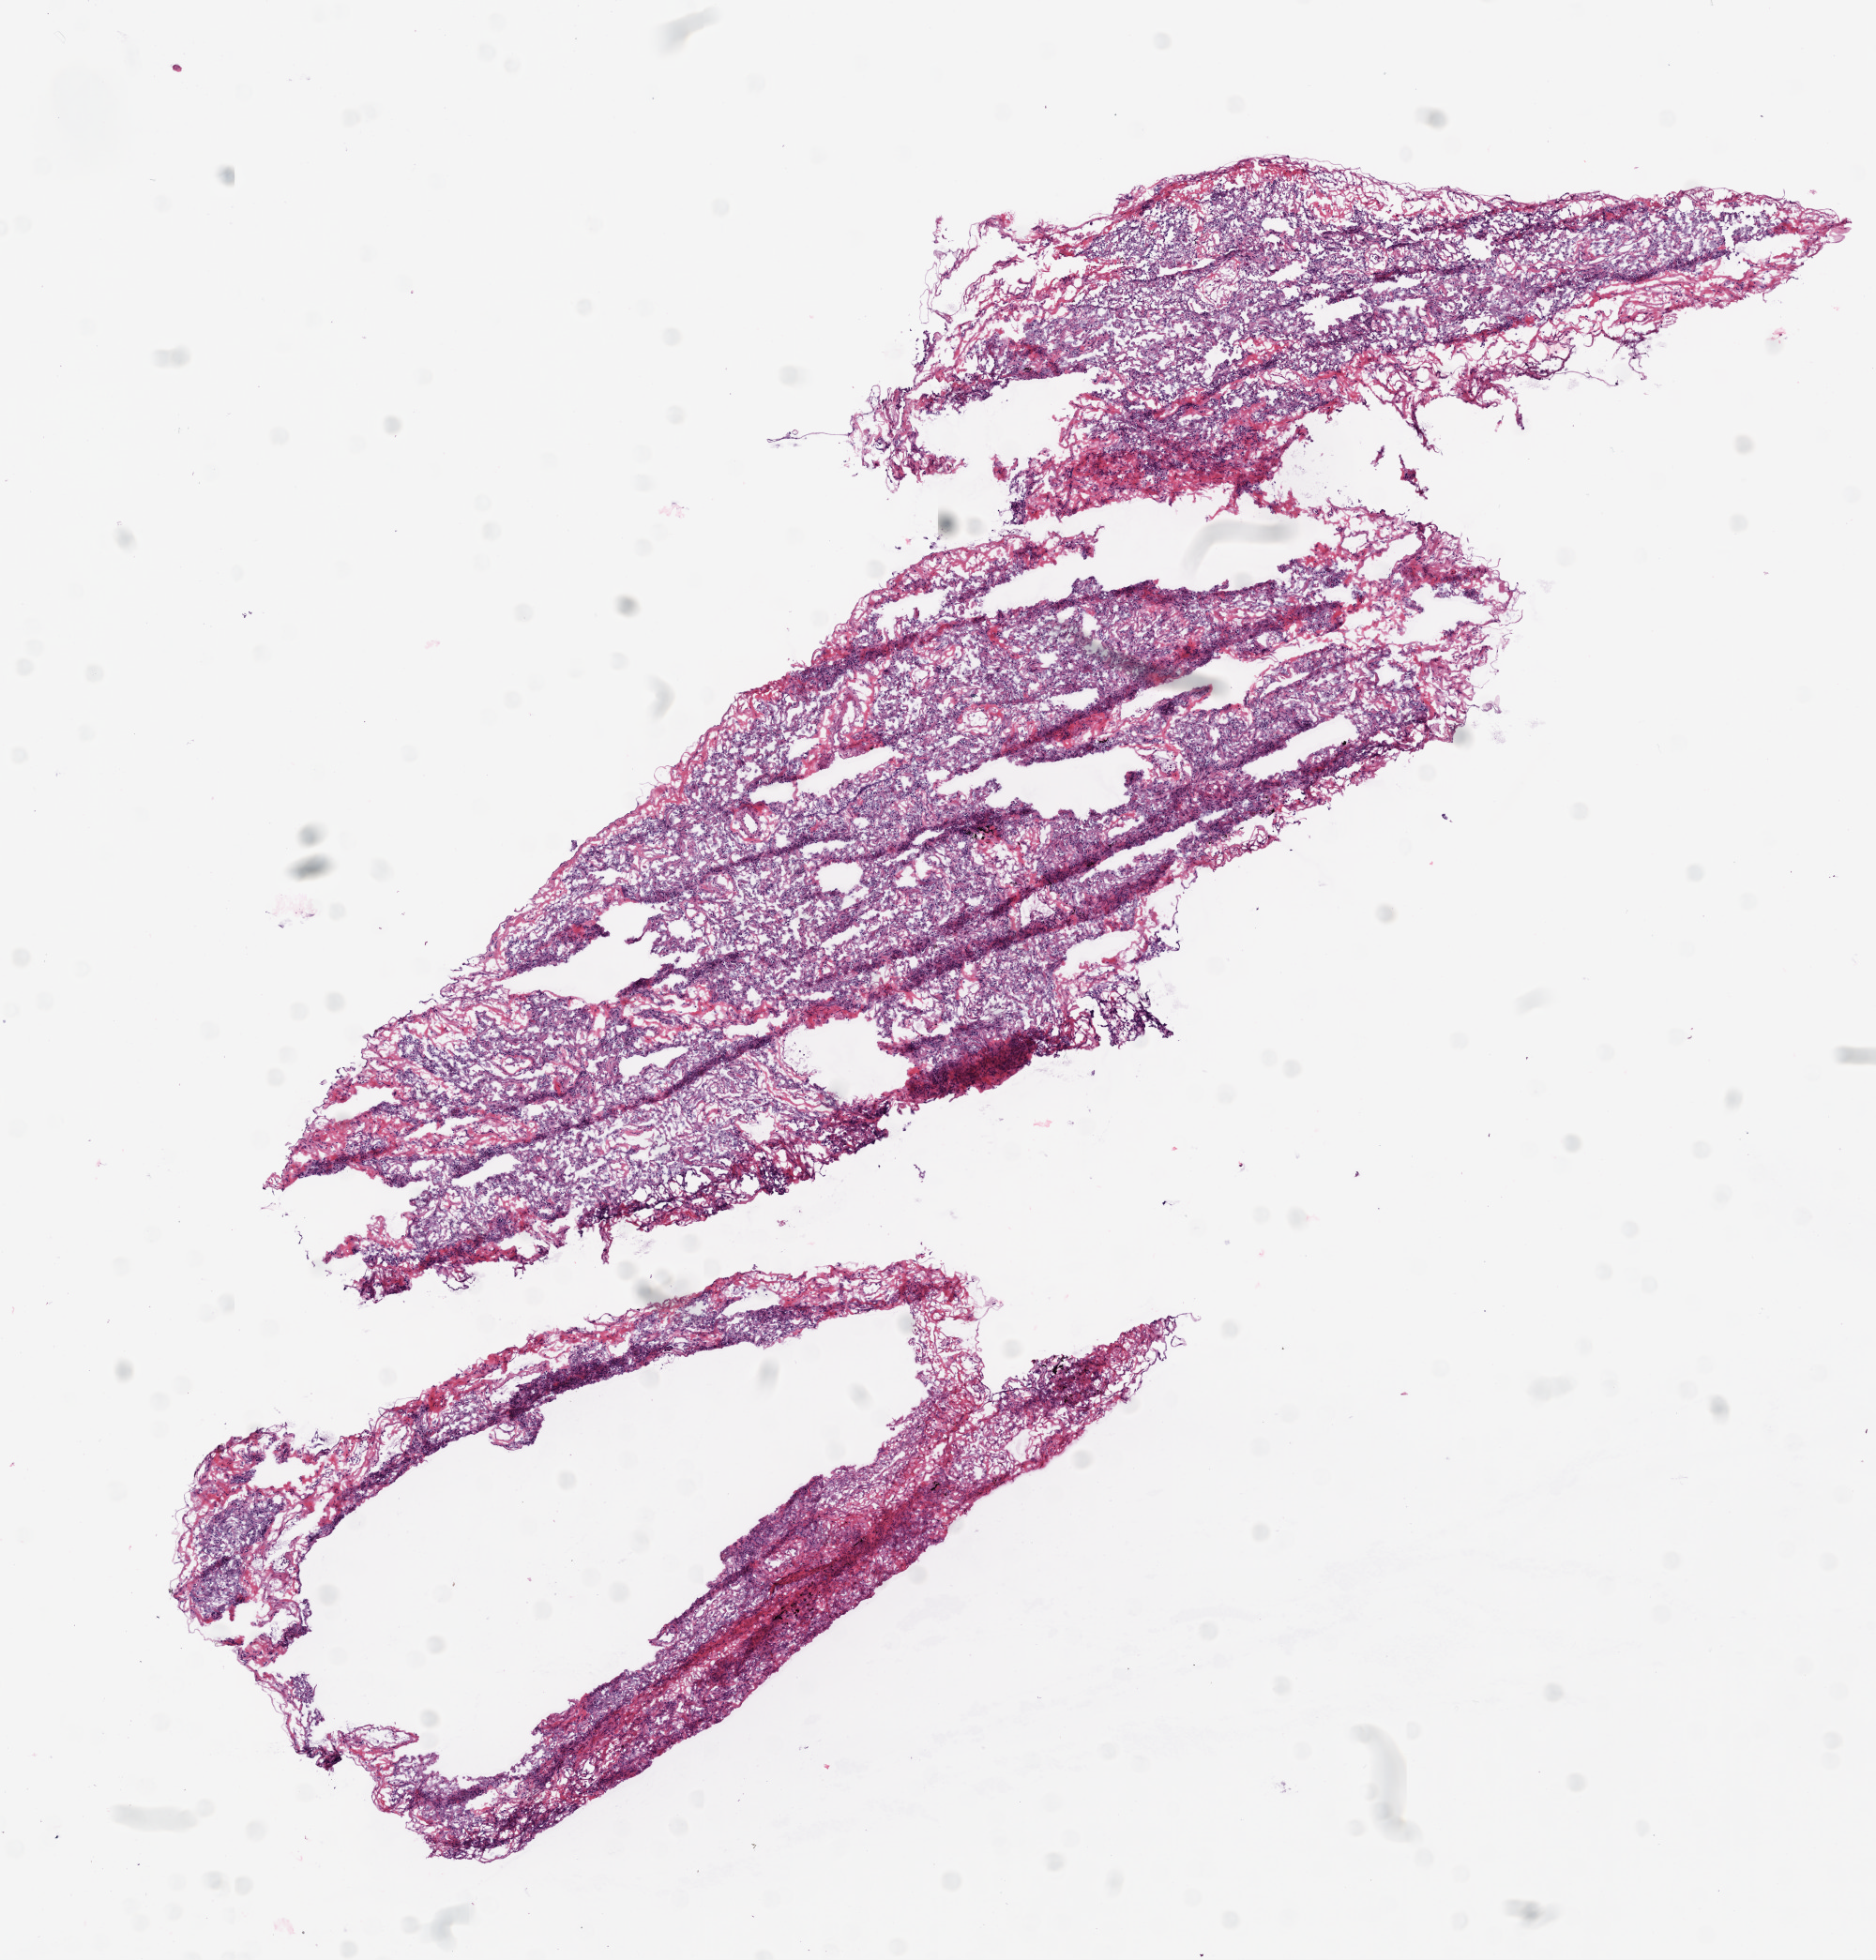
Whole-slide histology image, H&E-stained — a low-resolution overview of the entire scanned area, about 8.0 x 8.4 mm (from a 20x scan); frozen section; sample: solid tissue normal (non-tumour tissue), lung. Male patient; age at initial diagnosis 57 years.
This section: solid tissue normal (non-tumour) sample from the same patient. Patient diagnosis: Squamous cell carcinoma, NOS (upper lobe, lung).